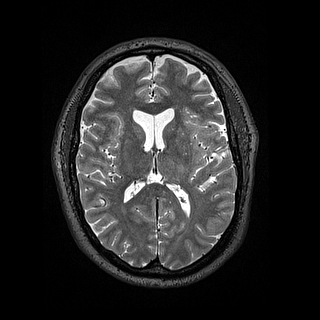
Brain MRI from a brain-tumour surgery series, one axial slice. Position 76 of 144 along the scan axis. 1.2 mm slice thickness. 320 × 320 image matrix. From the clinical record (not read from this slice): histopathology: Astrocytoma; WHO grade: 2.
Structures marked on this image (manually delineated by an expert):
- tumour: bounding box [x1, y1, x2, y2] px = [195, 155, 208, 171]